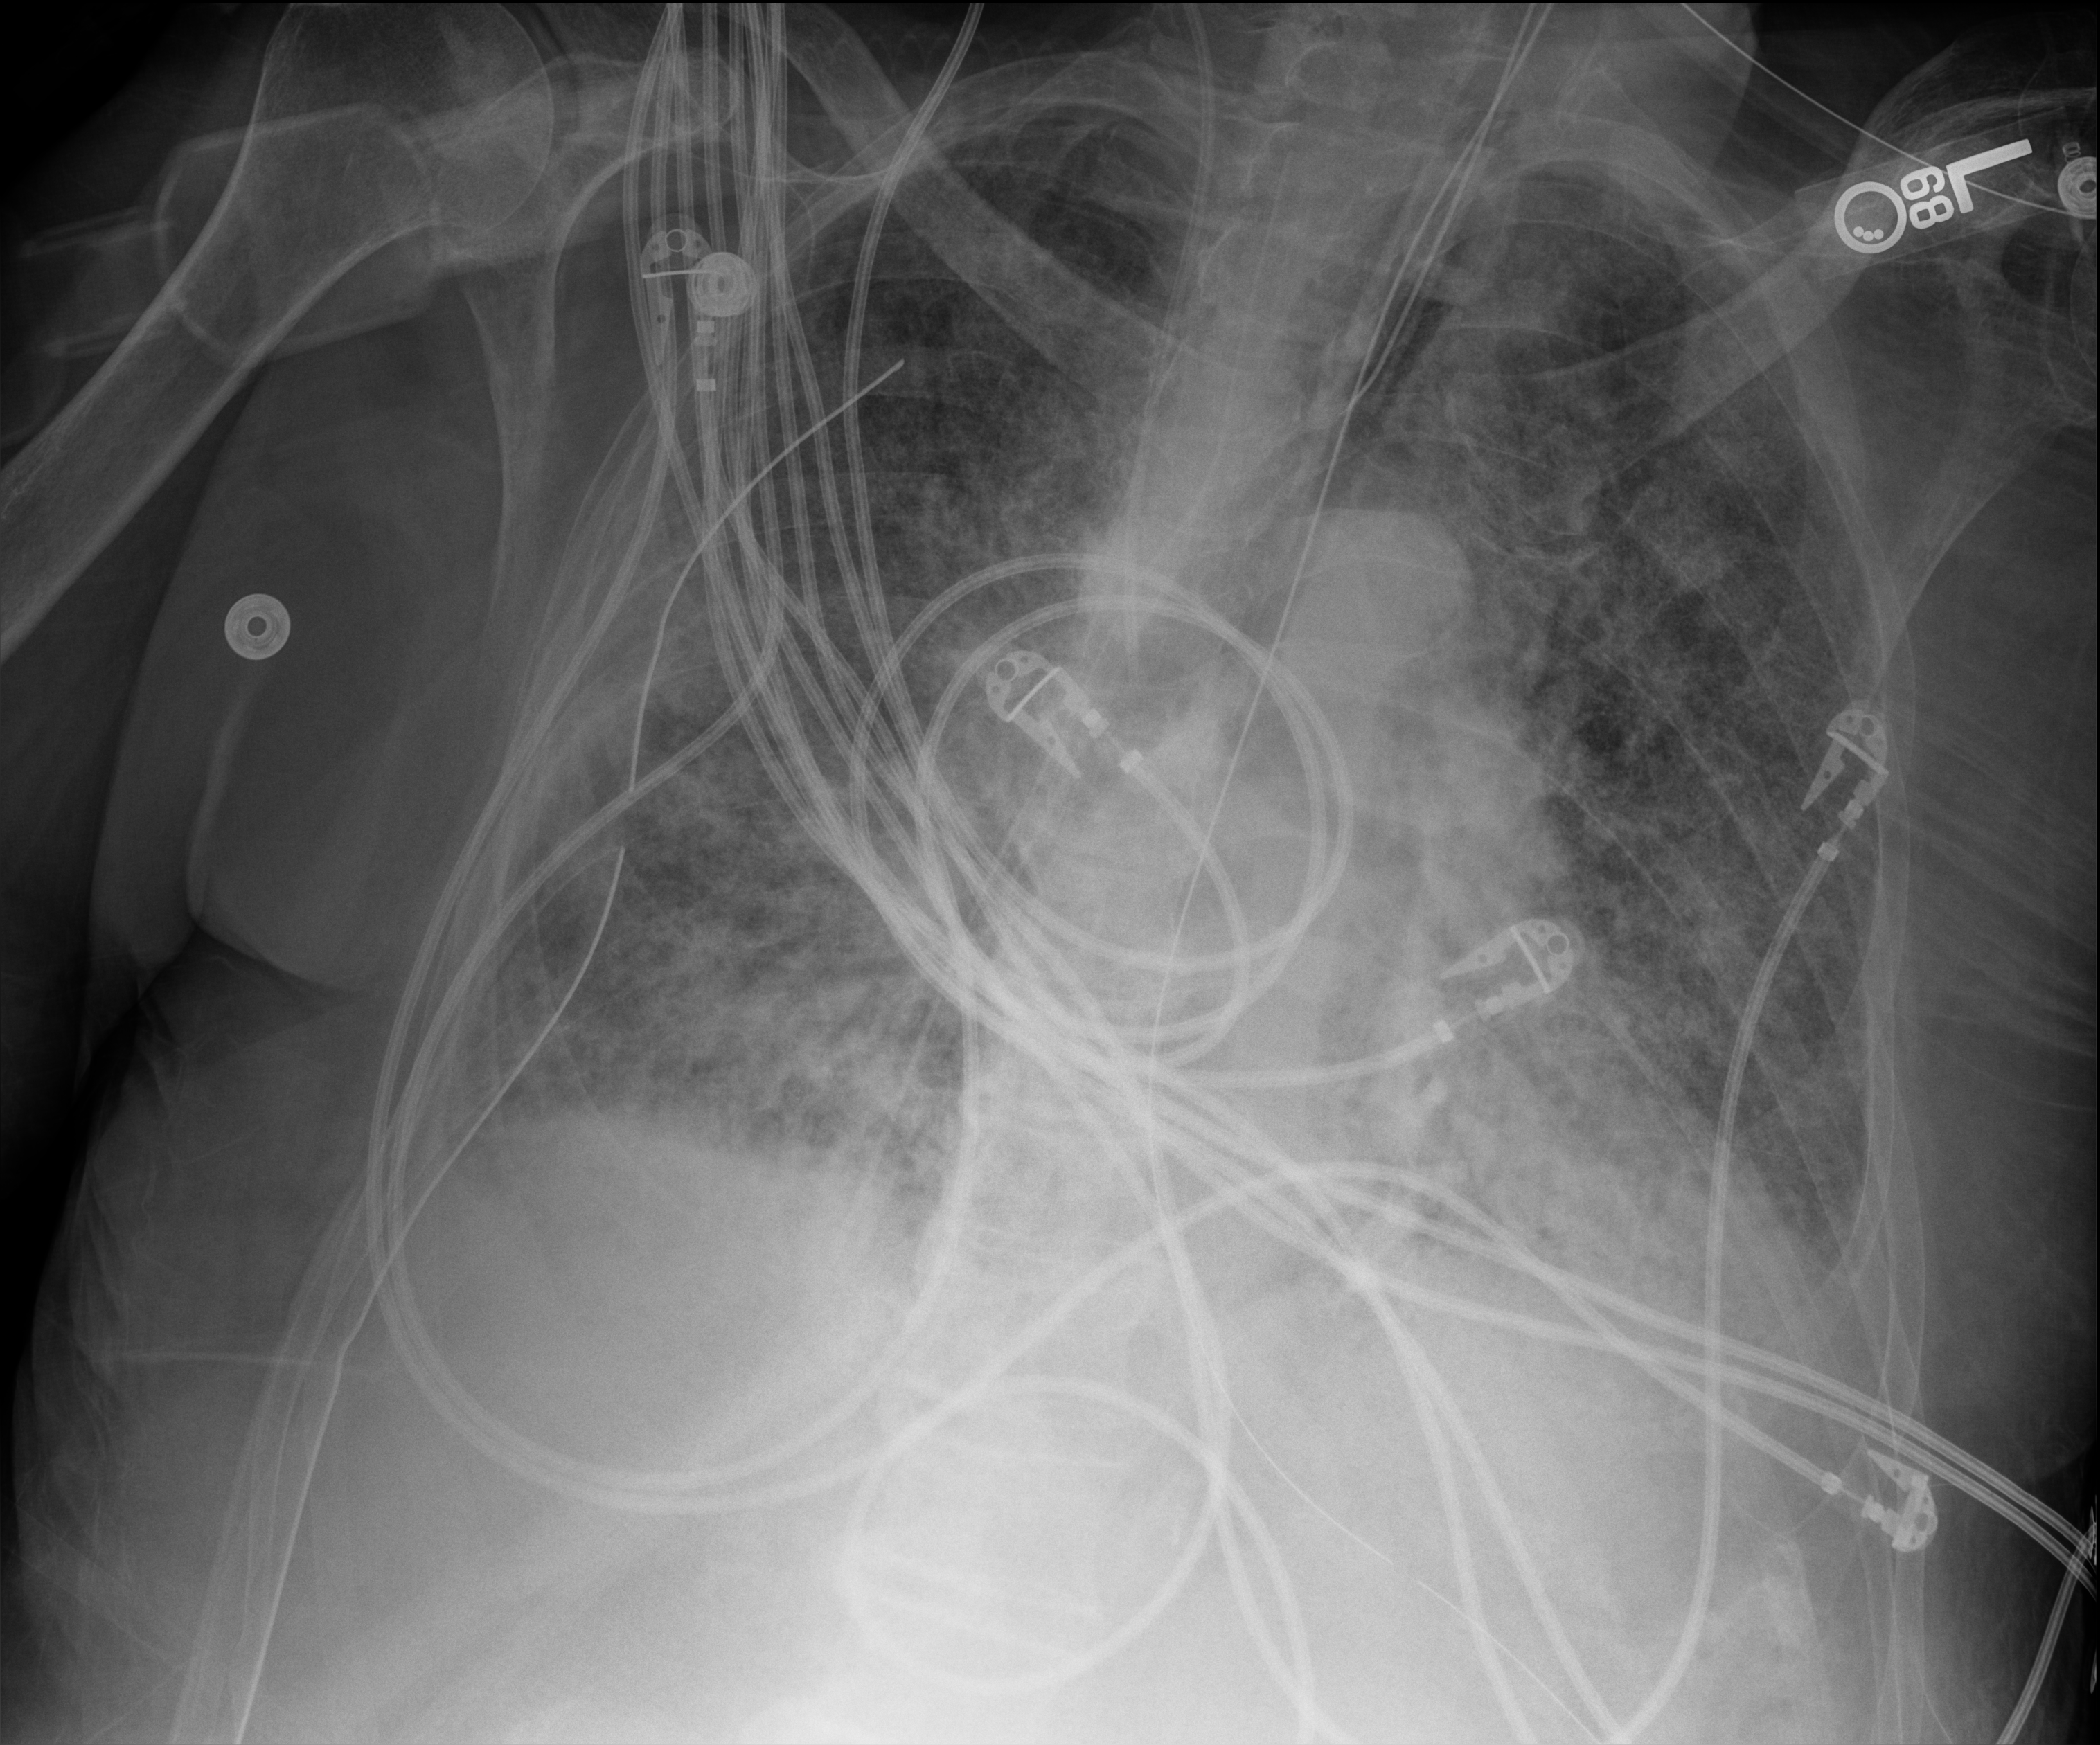
Portable chest radiograph, anteroposterior (AP) projection. Male patient hospitalised with COVID-19, age 75–90 years.
Hospital-stay facts (about this admission, not read from this image; timing relative to this image not recorded):
- diabetes (admission record): no
- mechanically ventilated during this hospital stay: yes